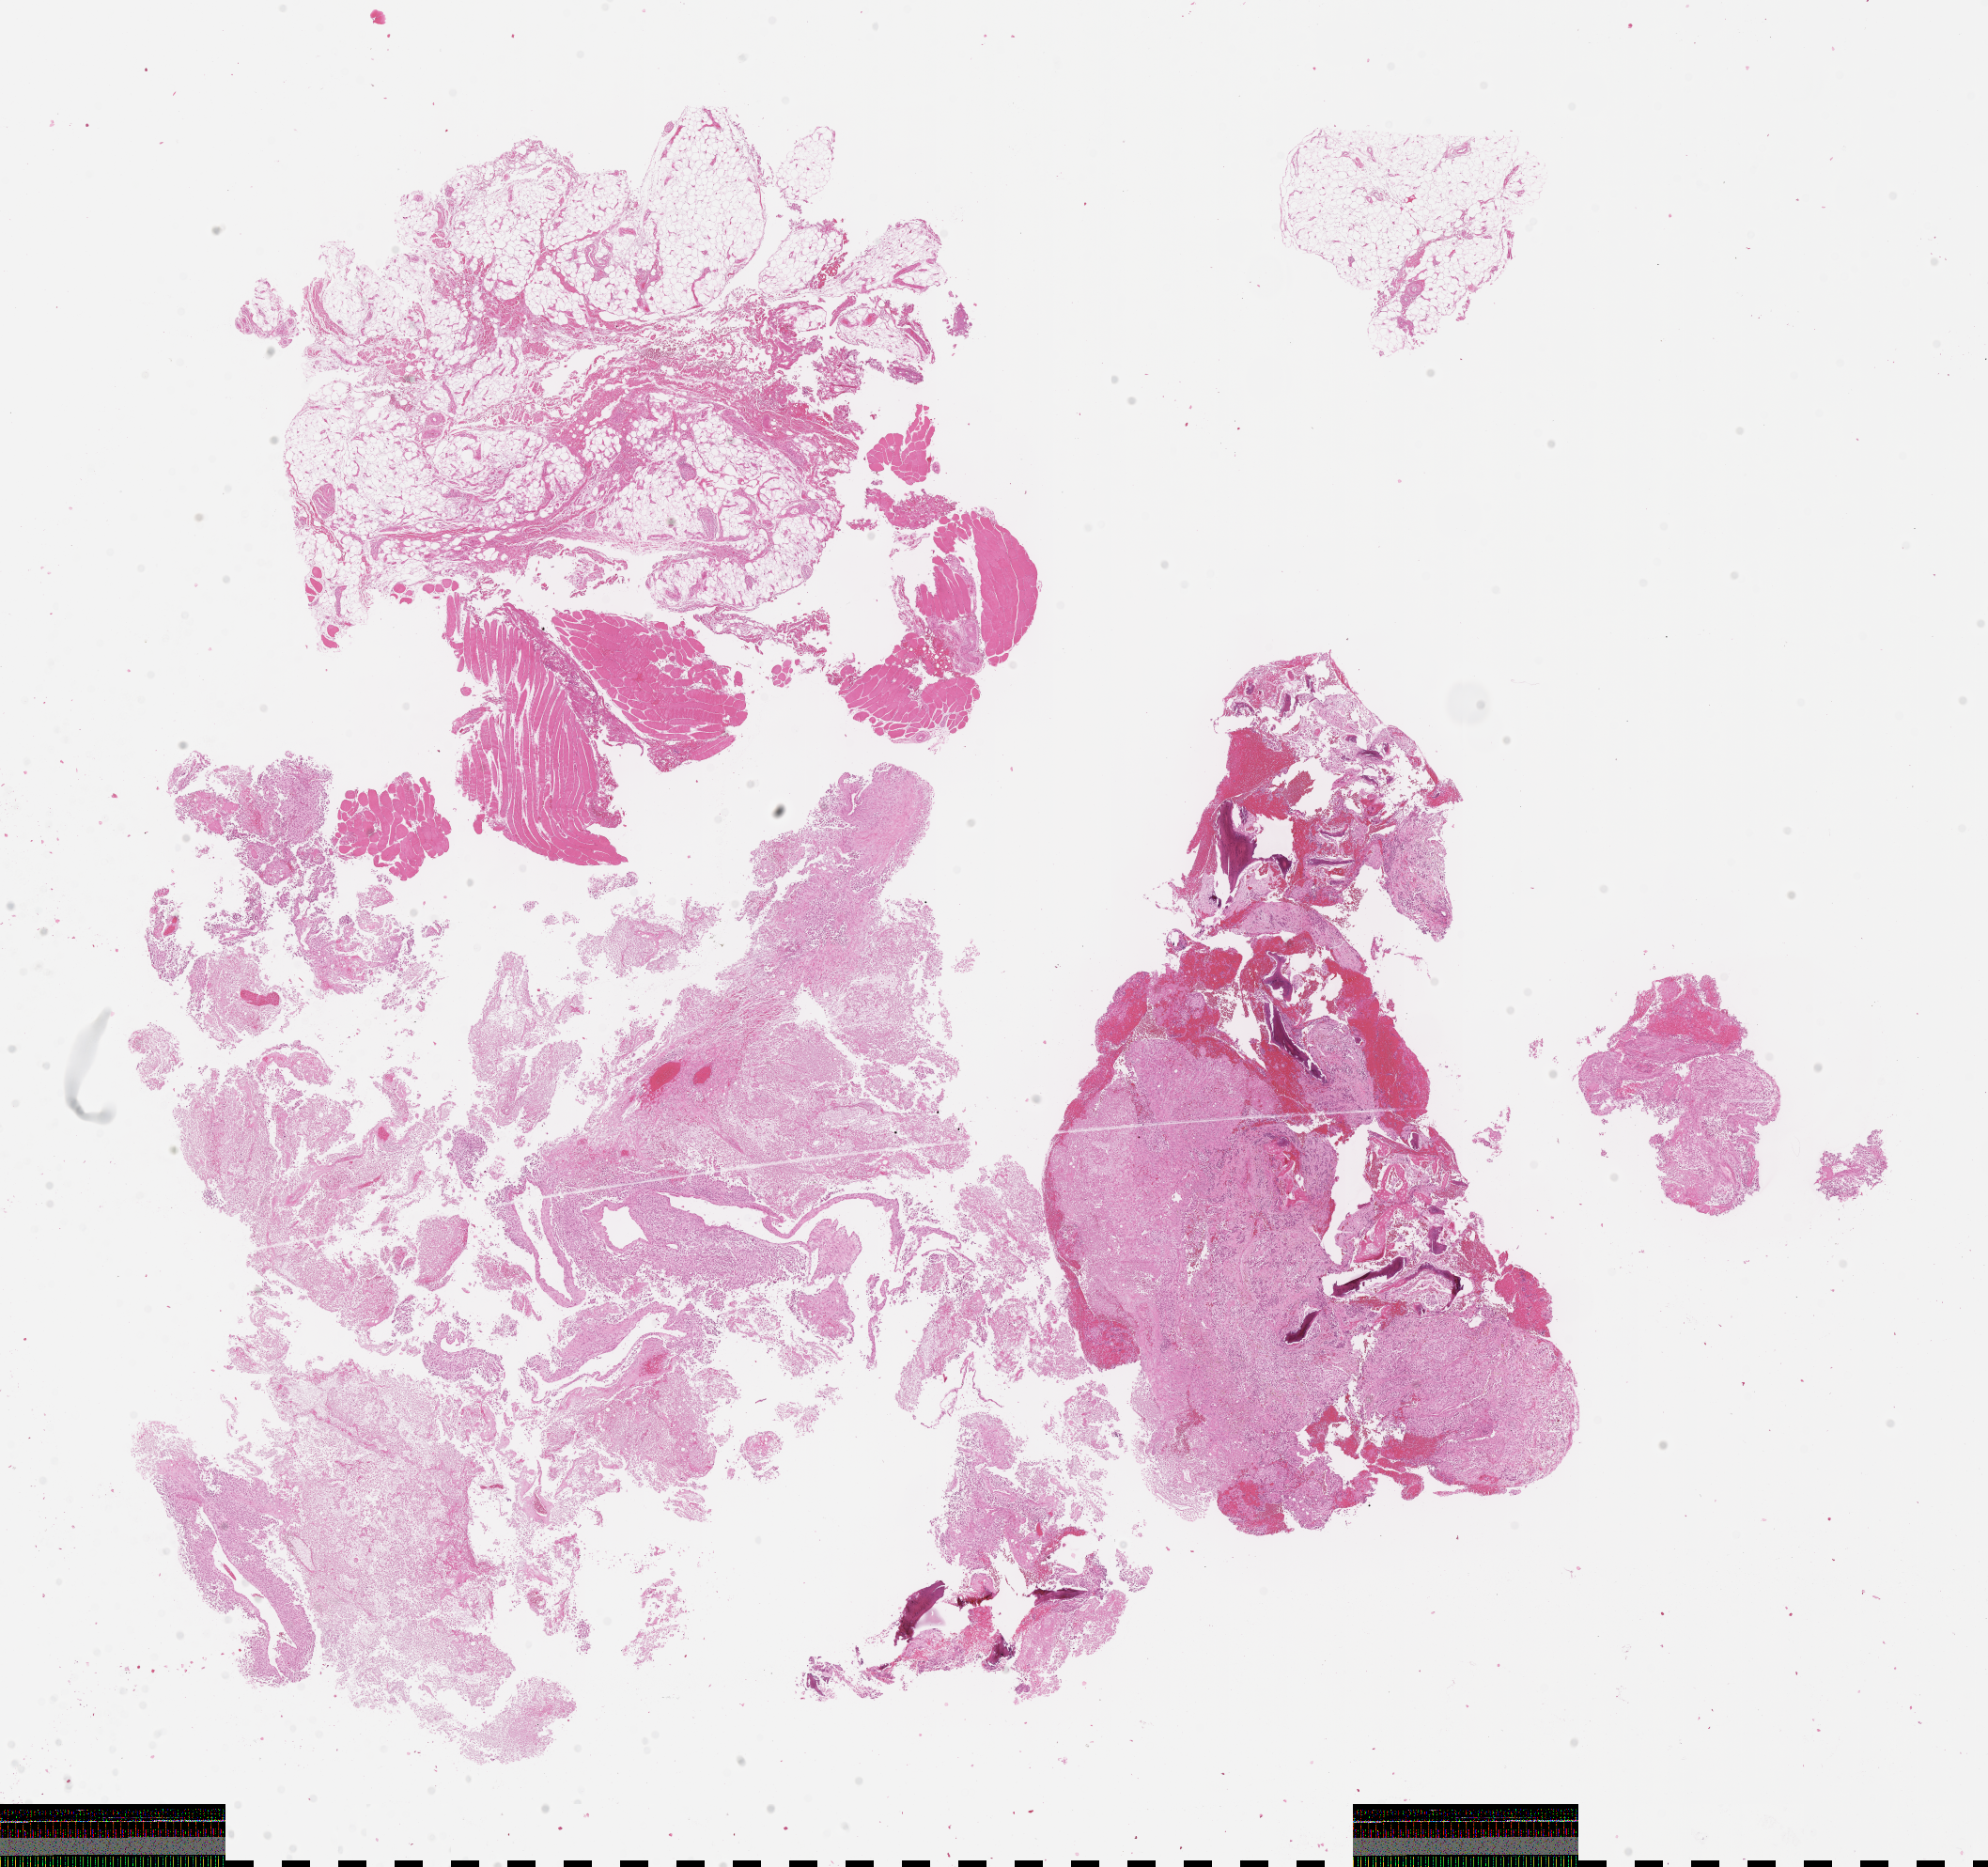
Whole-slide image, H&E stain of tumor tissue, a low-resolution overview of the entire scanned area, about 17.1 x 16.1 mm. Formalin-fixed paraffin-embedded section. Sample anatomic site: bone - femur, right distal. Patient: male, age 14.9 years at diagnosis.
* diagnosis: rhabdomyosarcoma; histological classification: alveolar rhabdomyosarcoma
* stage (as recorded): 4